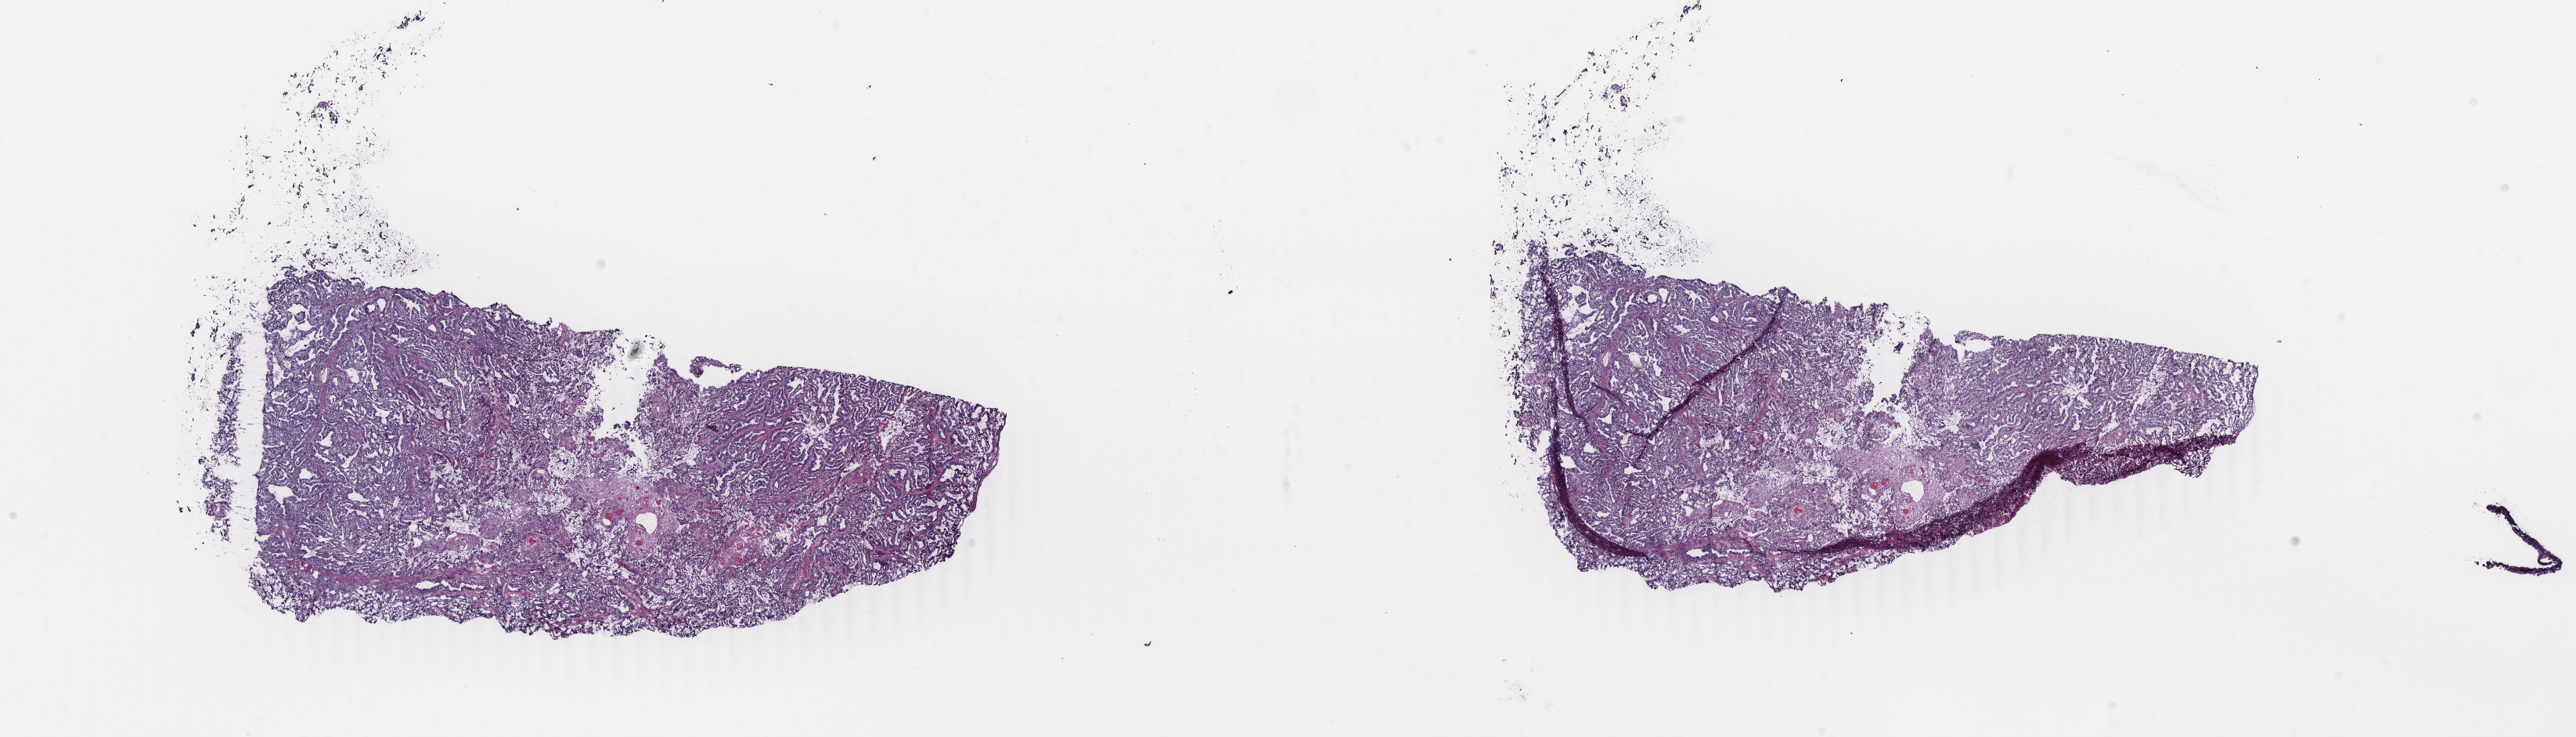
Digitized H&E-stained tissue section (whole slide), a low-resolution overview of the entire scanned area, about 26.2 x 7.5 mm; frozen section from the bottom of the tissue portion; sample: primary tumour, uterus. Patient: female, age at initial diagnosis 61 years. Histologic grade: G1 (well differentiated). Pathologist review of this section (percent, as recorded): tumour cells 100%, tumour nuclei 85%, normal cells 0%, stromal cells 0%, necrosis 0%. Inflammatory infiltration, as recorded: lymphocyte infiltration 0%, monocyte infiltration 0%, neutrophil infiltration 0%.
* pathologic diagnosis: Endometrioid adenocarcinoma, NOS (endometrium)
* FIGO stage: IA